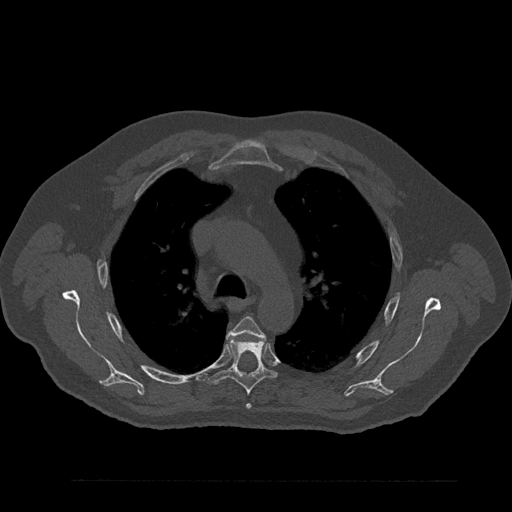
CT including the spine, one axial slice. Position 610 of 797 along the scan axis. Reconstruction kernel Br40s/3. 120 kVp. Bone window (W 1800 / L 400 HU). 0.5 mm slice thickness. 512 × 512 image matrix. Patient: male, 61 years. From the clinical record (not read from this slice): primary cancer: prostate.
Outlined on this slice (semi-automatic segmentation, software-assisted and operator-edited):
- T4 vertebra: bounding box [x1, y1, x2, y2] px = [228, 317, 266, 409]
- T5 vertebra: [208, 339, 276, 395]